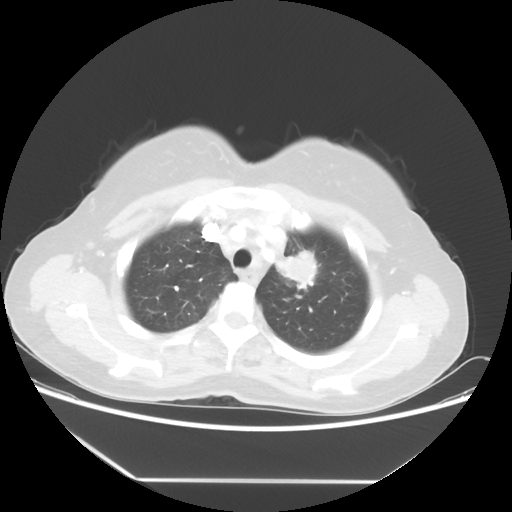
Chest CT, one axial slice. Position 43 of 52 along the scan axis. Reconstruction kernel STANDARD. 100 kVp. Lung window (W 1500 / L -600 HU). 5 mm slice thickness. 512 × 512 image matrix, field of view 390 × 390 mm. Patient: female, 50 years. Case-level facts recorded for this patient, not image findings: clinical TNM (as recorded): T2 N3 M0.
Outlined on this slice (bounding box drawn by a radiologist):
- lung tumour (recorded histology: adenocarcinoma): bounding box [x1, y1, x2, y2] px = [272, 242, 326, 293]